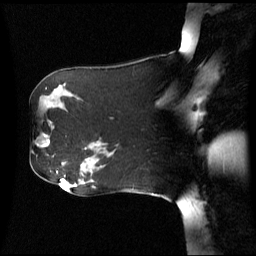
Breast MRI (dynamic contrast-enhanced), one sagittal slice. Position 37 of 60 along the scan axis. Dynamic contrast-enhanced series, image 2 of 3 at this slice position (ordered by acquisition). 1.5 T. TE 4.2 ms, TR 8.4 ms. 2.5 mm slice thickness. 256 × 256 image matrix, field of view 260 × 260 mm. Patient: female, 62 years. Case-level facts recorded for this patient, not image findings: setting: breast cancer imaged before/during neoadjuvant chemotherapy; receptor status: HR-positive, HER2-negative.
Annotated regions visible in this slice (semi-automatically segmented with operator editing):
- analysis volume of interest (the breast-tissue region the enhancement analysis was run in; not a lesion): bounding box (x1, y1, x2, y2) in pixels: (31, 120, 57, 159)
- tumour enhancement mask (voxels above the 70 % enhancement threshold inside the analysis volume of interest): (43, 142, 50, 148)